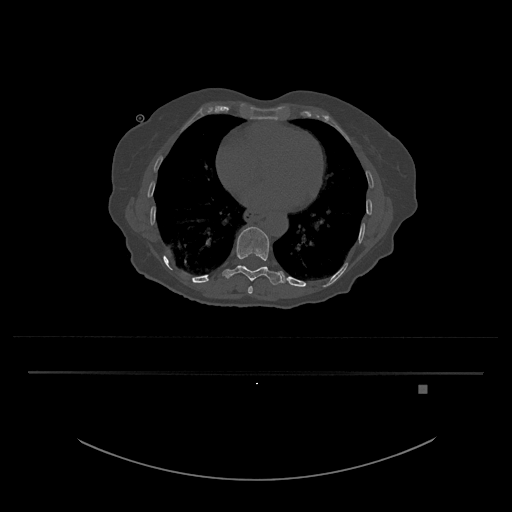
CT including the spine, one axial slice; slice 715 of 797 in the series (ordered by position); reconstruction kernel Br40s/3; 120 kVp; bone window (W 1800 / L 400 HU); 0.5 mm slice thickness; 512 × 512 image matrix, field of view 500 × 500 mm. Female patient, age 57 years. From the clinical record (not read from this slice): primary cancer: cervical.
Outlined on this slice (semi-automatically segmented with operator editing):
- T10 vertebra: box from (x=222, y=227) to (x=285, y=285) px
- T9 vertebra: (x=248, y=286)–(x=253, y=294)